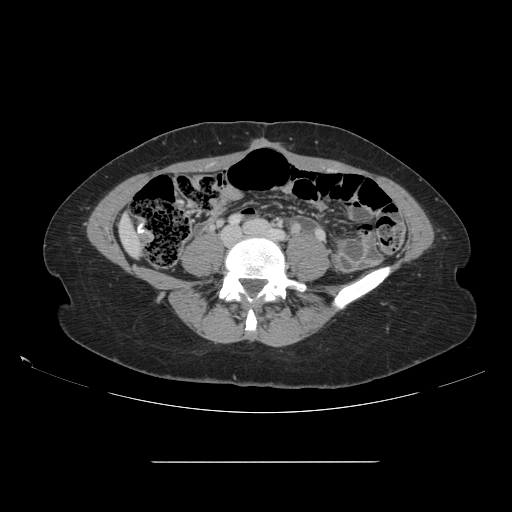
Contrast-enhanced abdominal CT, one axial slice; position 9 of 151 along the scan axis; 120 kVp; intravenous contrast given; soft-tissue window (W 400 / L 40 HU); 2.5 mm slice thickness; 512 × 512 image matrix, field of view 421 × 421 mm. Female patient, age 46 years. Case-level facts recorded for this patient, not image findings: diagnosis: colorectal cancer liver metastases, imaged before liver resection; multiple liver metastases: yes; largest metastasis: 3 cm; disease in both lobes: yes.
Outlined on this slice (expert manual segmentation):
- liver: bounding box <121,220,141,255> (left, top, right, bottom; pixels)
- planned liver remnant (the part of the liver to remain after resection): <121,220,142,255>